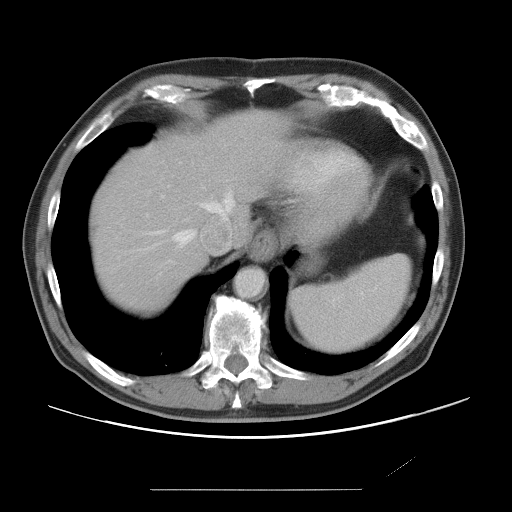
Contrast-enhanced abdominal CT, one axial slice; position 63 of 87 along the scan axis; intravenous contrast given; soft-tissue window (W 400 / L 40 HU); 5 mm slice thickness; 512 × 512 image matrix. Male patient, age 74 years. From the clinical record (not read from this slice): diagnosis: colorectal cancer liver metastases, imaged before liver resection; multiple liver metastases: yes; largest metastasis: 1.1 cm; chemotherapy before resection: yes.
Structures marked on this image (outlined manually by an expert reader):
- hepatic veins: bounding box <153,196,234,245> (left, top, right, bottom; pixels)
- liver: <90,112,283,310>
- planned liver remnant (the part of the liver to remain after resection): <90,112,284,311>